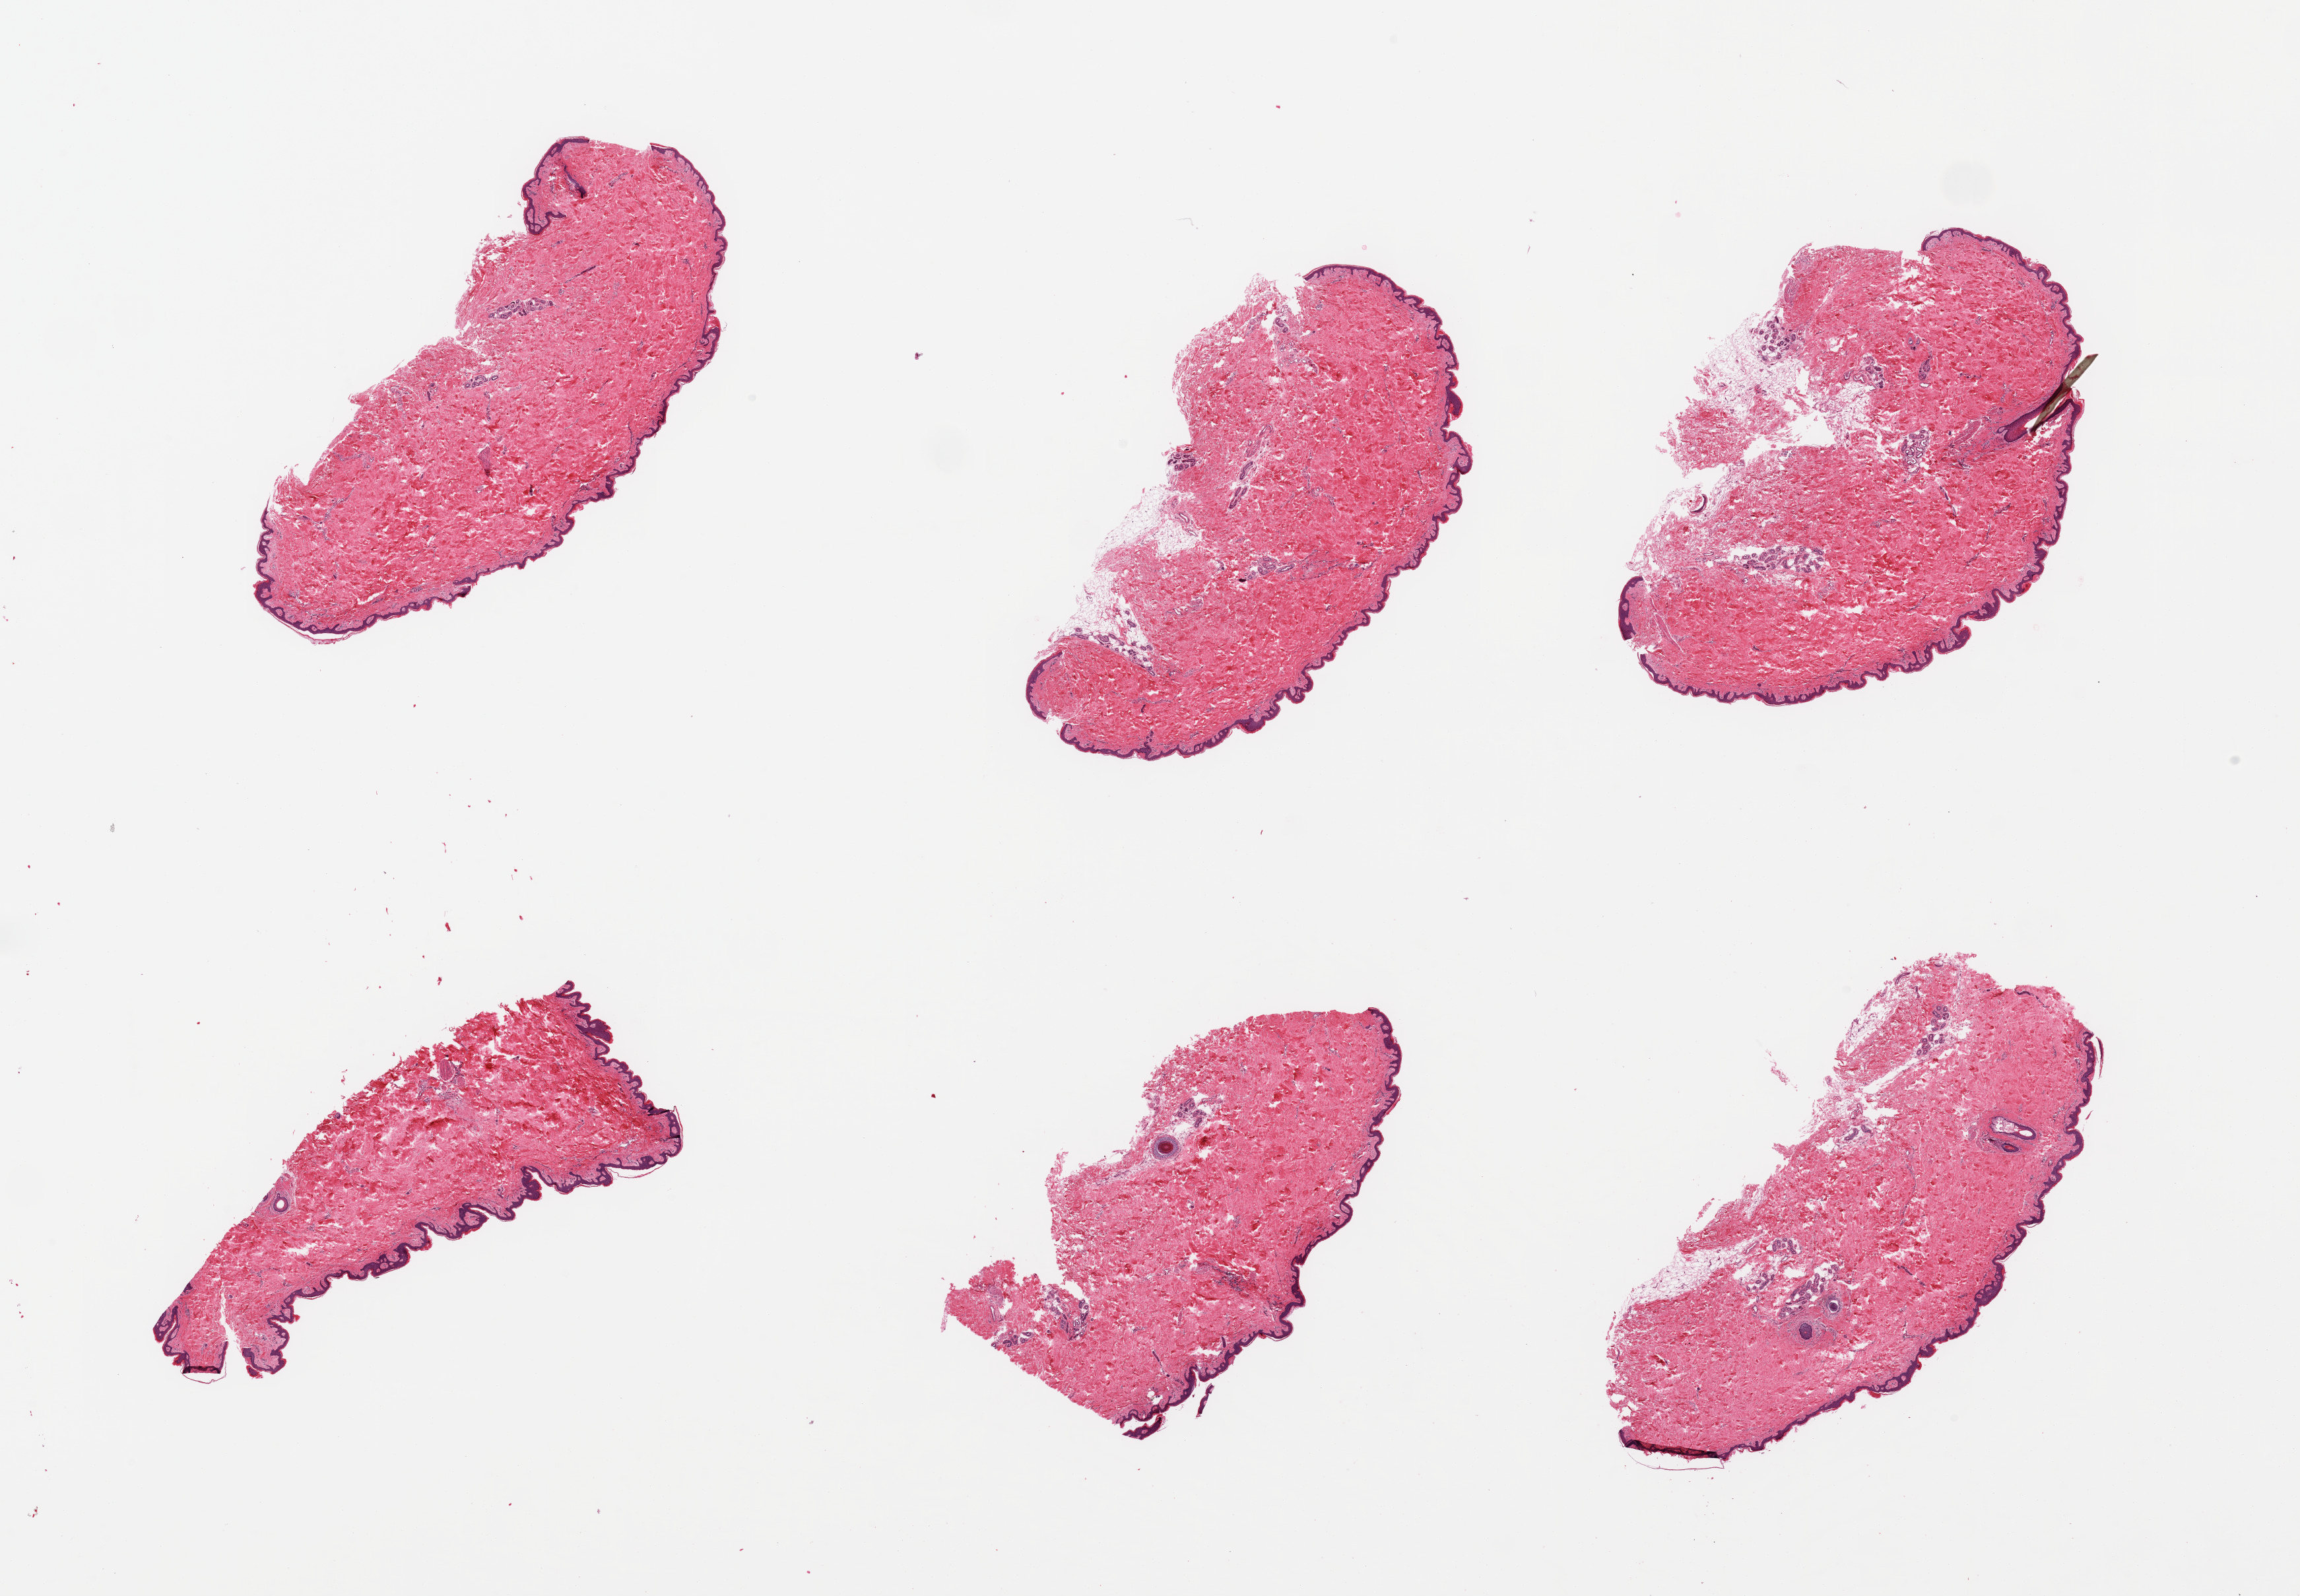
Digitized hematoxylin and eosin (H&E)-stained section, shown as a low-resolution overview of the whole scanned area (about 27.6 x 19.1 mm), PAXgene-fixed, paraffin-embedded tissue, section of skin of suprapubic region (target tissue), tissue donor sample. Male donor.
Reviewer comment on this tissue sample: 6 pieces; well trimmed; <10% dermal fat.